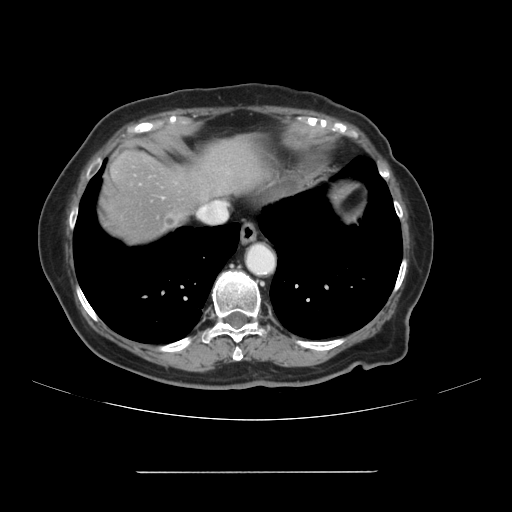
Contrast-enhanced abdominal CT, one axial slice; slice 99 of 111 in the series (ordered by position); 120 kVp; intravenous contrast given; soft-tissue window (W 400 / L 40 HU); 512 × 512 image matrix. Female patient, age 74 years. From the clinical record (not read from this slice): diagnosis: colorectal cancer liver metastases, imaged before liver resection; multiple liver metastases: yes; largest metastasis: 1.1 cm; disease in both lobes: yes.
Outlined on this slice (manually delineated by an expert):
- liver: bounding box [x1, y1, x2, y2] px = [98, 138, 270, 247]
- planned liver remnant (the part of the liver to remain after resection): [199, 138, 270, 196]
- liver metastasis: [166, 215, 176, 225]